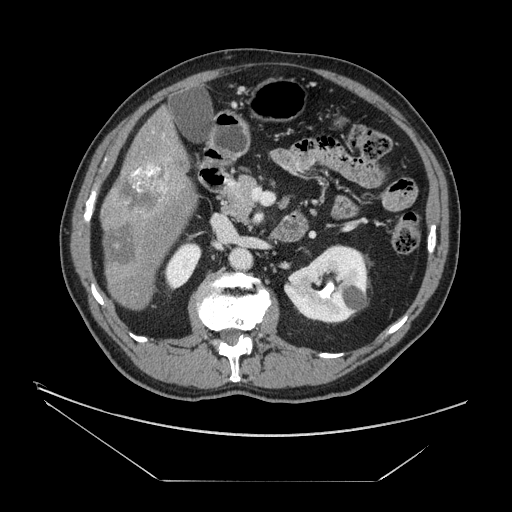
Contrast-enhanced abdominal CT, one axial slice. Position 67 of 161 along the scan axis. Reconstruction kernel STANDARD. 120 kVp. Intravenous contrast given. Soft-tissue window (W 400 / L 40 HU). 2.5 mm slice thickness. 512 × 512 image matrix, field of view 440 × 440 mm. Male patient, age 65 years. From the clinical record (not read from this slice): diagnosis: colorectal cancer liver metastases, imaged before liver resection; multiple liver metastases: yes; largest metastasis: 4.2 cm; disease in both lobes: yes.
Structures marked on this image (manually delineated by an expert):
- liver: box from (x=102, y=110) to (x=197, y=310) px
- portal vein (with intrahepatic branches): (x=131, y=165)–(x=169, y=193)
- liver metastasis: (x=107, y=228)–(x=137, y=265)
- liver metastasis: (x=117, y=165)–(x=172, y=214)